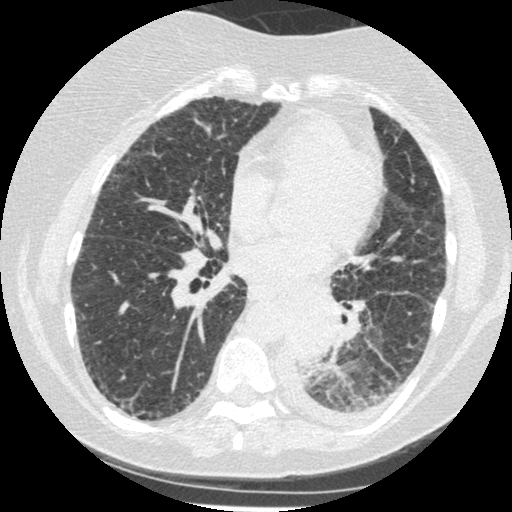
Chest CT (low-dose screening protocol), one axial image; third annual screen; lung window (W 1500 / L -600 HU); standard (soft-tissue) reconstruction kernel (STANDARD); slice 239 of 341 in the series; 512 × 512 image matrix, field of view 310 × 310 mm. Female, age 60 years at enrolment. Former smoker at enrolment.
Expert reader's lesion annotation, bounding box <276,303,343,375> (left, top, right, bottom; pixels). The exam's reader record, not a measurement of the box and not confirmed to be the same lesion: non-calcified nodule or mass ≥4 mm, left lower lobe, 54 × 38 mm, smooth margins, soft tissue attenuation, pre-existing on the prior screen: yes; interval growth: yes. Official screen result: positive, other. Participant outcome: lung cancer diagnosed 15 days after this screen — small cell carcinoma, NOS, left lower lobe, undifferentiated (G4), stage IV (AJCC 6th edition), 69 mm at pathology.